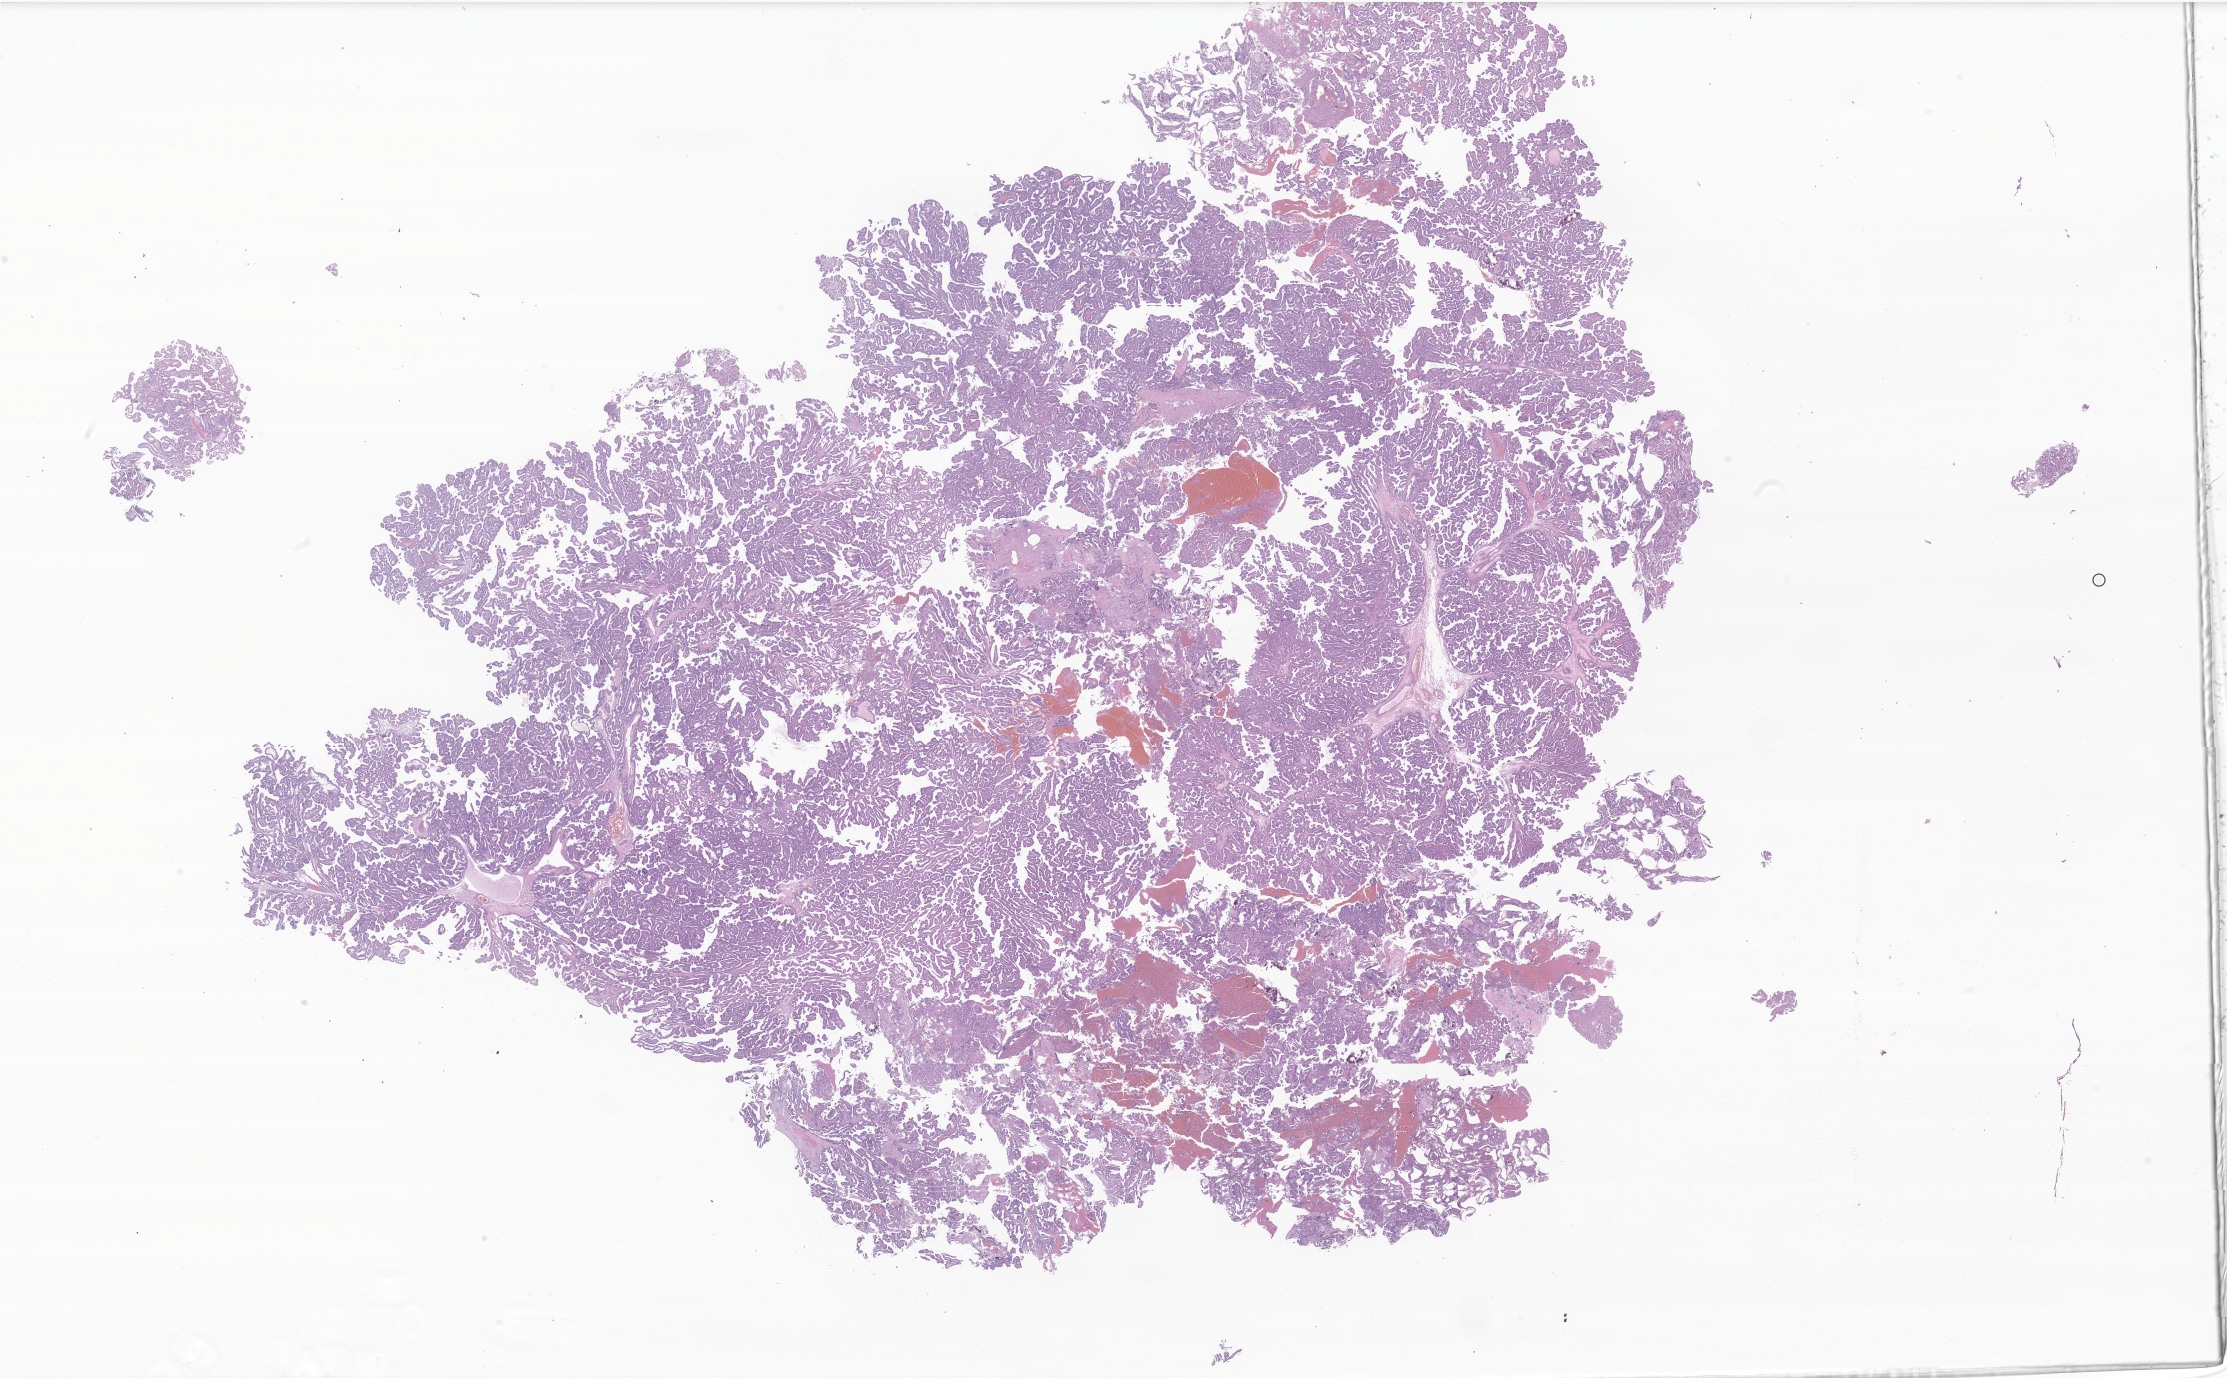
Digitized hematoxylin and eosin (H&E)-stained section of tumor tissue from the brain, a low-resolution overview of the entire scanned area, about 37.6 x 23.2 mm, formalin-fixed, paraffin-embedded (FFPE) tissue. Patient: female, age 972 days.
Diagnosis: Atypical choroid plexus papilloma.